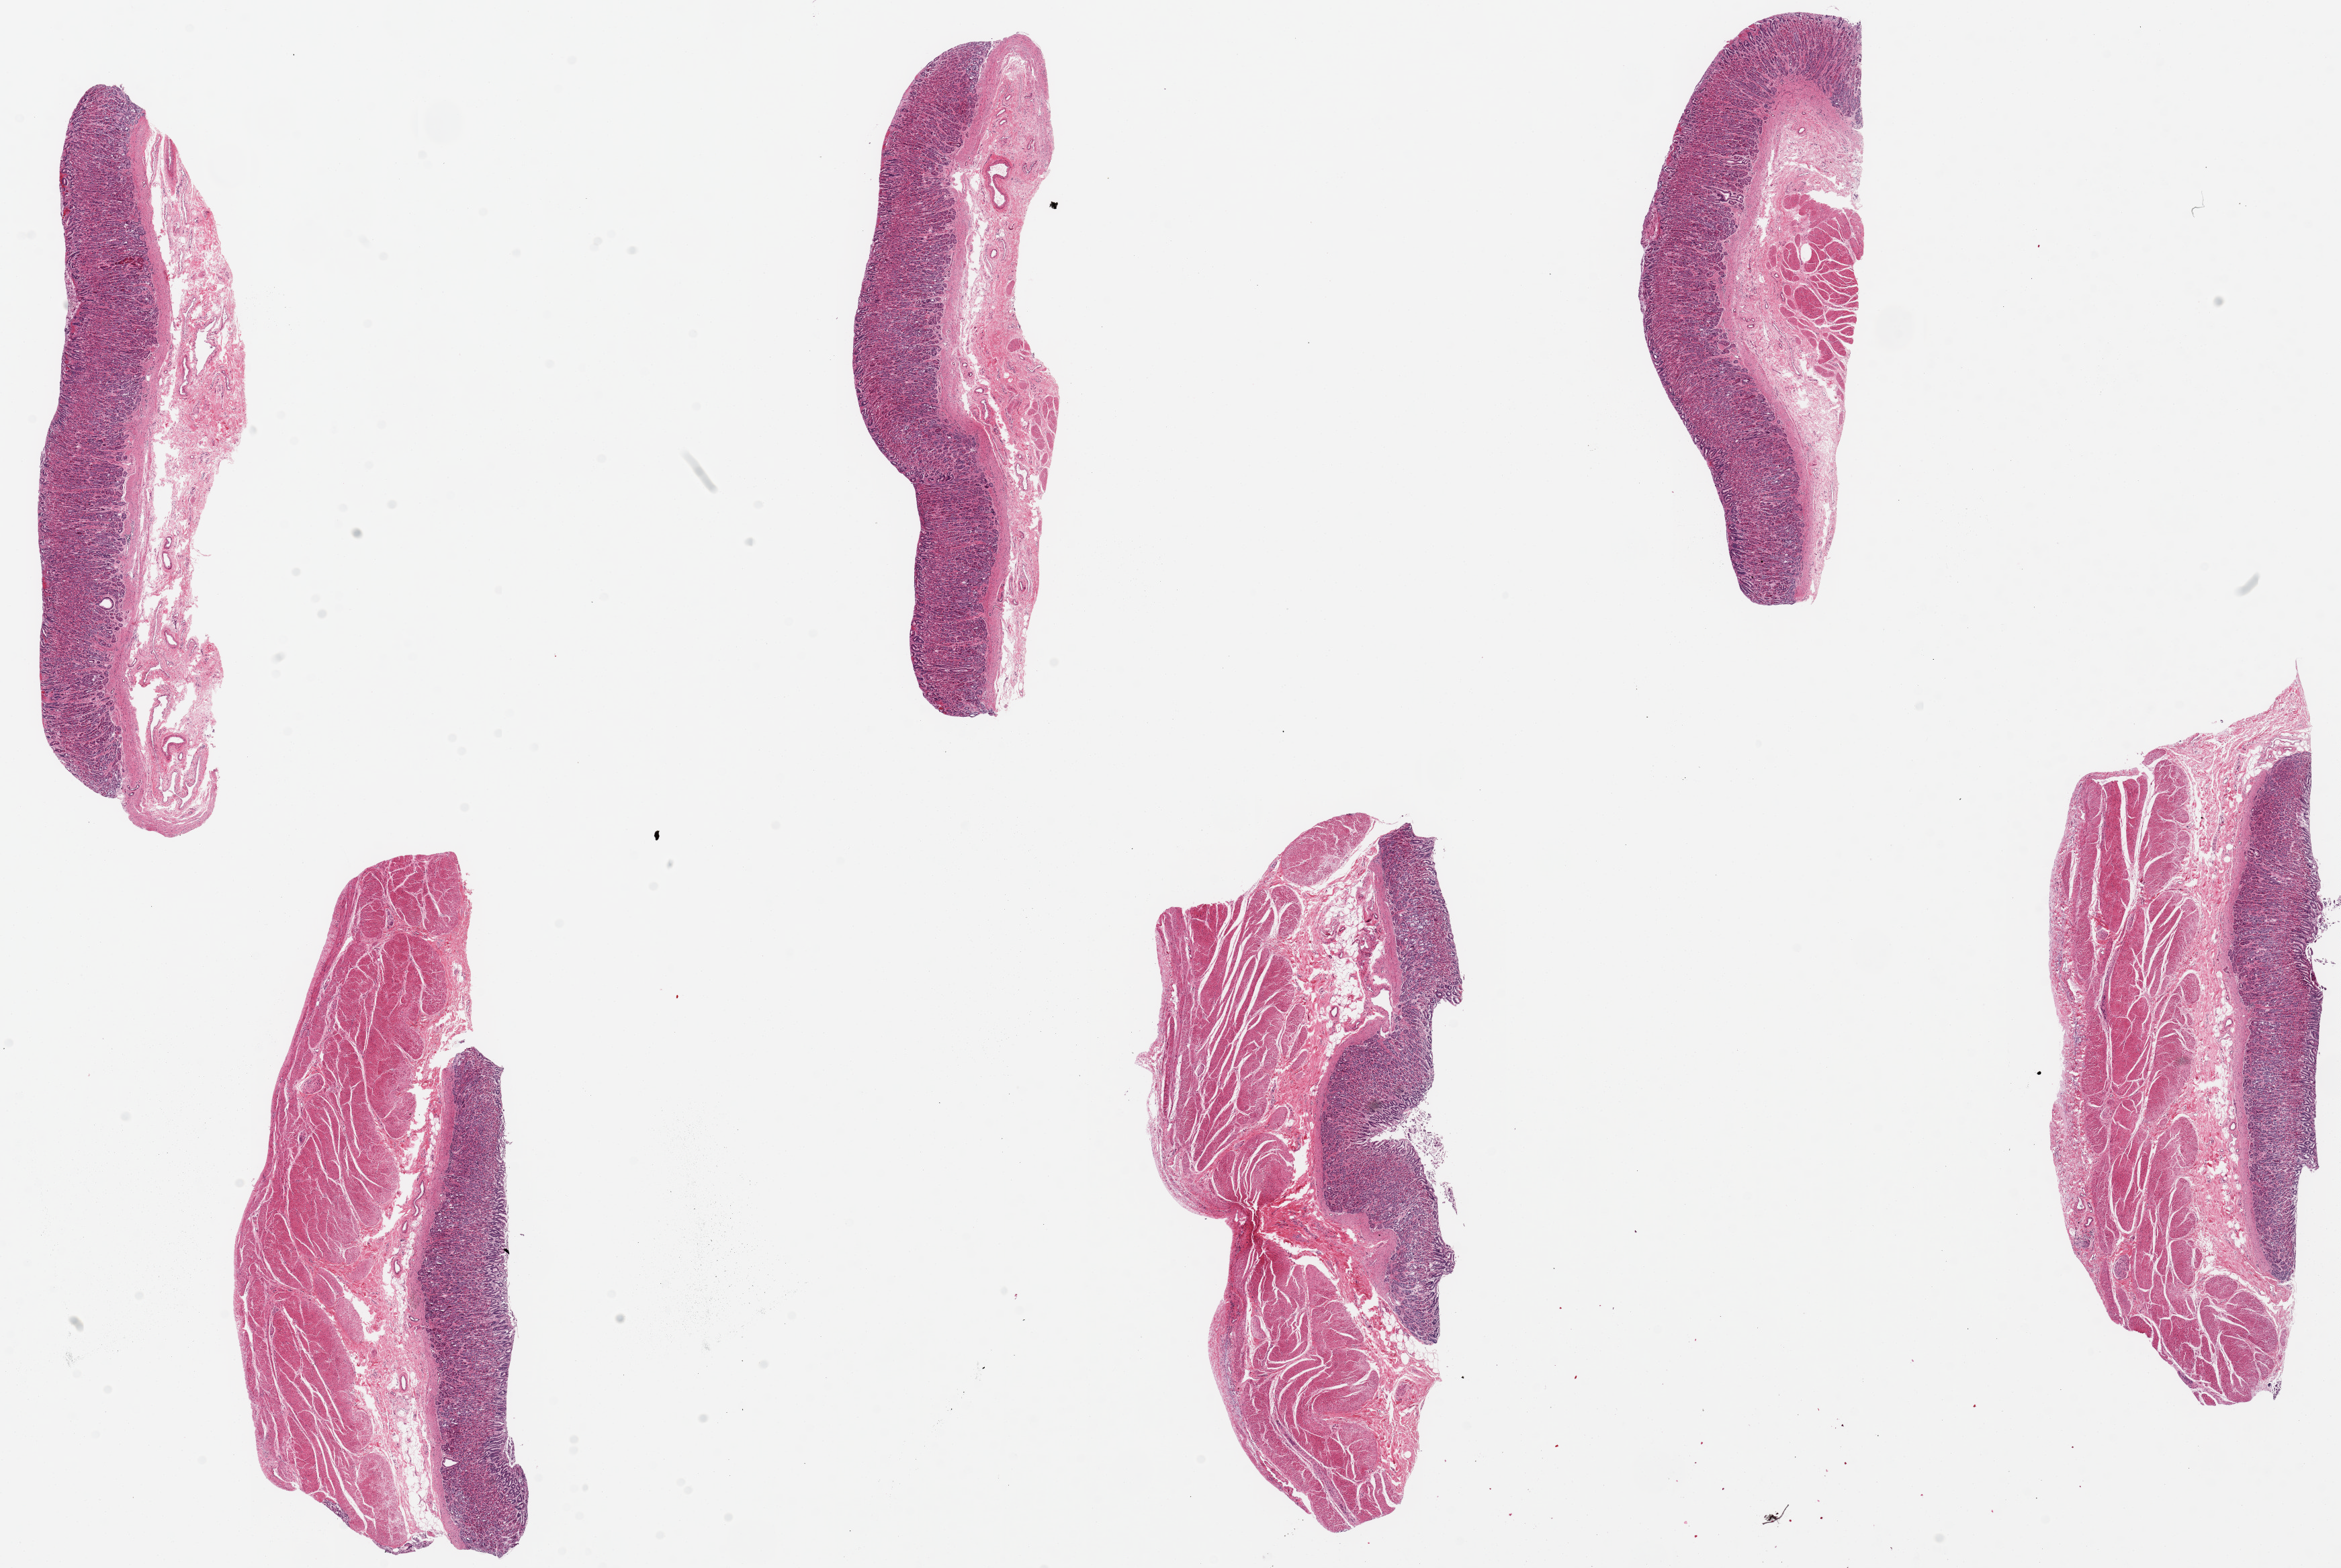
Hematoxylin and eosin (H&E) whole-slide image — shown as a low-resolution overview of the whole scanned area (about 27.6 x 18.5 mm). PAXgene-fixed, paraffin-embedded tissue. Sampled site (target tissue): stomach. Donor tissue sample. Male donor.
- pathologist's review note for this sample: 6 pieces, up to 9x3mm; excellent preservation; mucosa is ~30-60% of thickness